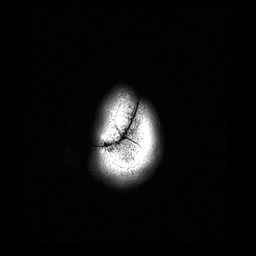
Brain MRI from a brain-tumour surgery series, one axial slice. Slice 2 of 44 in the series (ordered by position). 4 mm slice thickness. 256 × 256 image matrix, field of view 240 × 240 mm. Case-level facts recorded for this patient, not image findings: histopathology: Astrocytoma; WHO grade: 4; IDH mutation: yes.
Structures marked on this image (manually delineated by an expert):
- tumour: bounding box <111,145,115,149> (left, top, right, bottom; pixels)